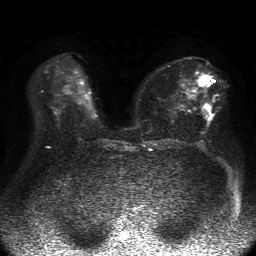
Breast MRI, one axial slice. Diffusion-weighted series; image 2 of 4 stored at this slice position (different b-values; order by instance number). 1.5 T. 4 mm slice thickness. 256 × 256 image matrix, field of view 360 × 360 mm. Female patient.
Structures marked on this image (outlined manually by an expert reader):
- tumour on diffusion-weighted imaging: box from (x=198, y=74) to (x=211, y=109) px